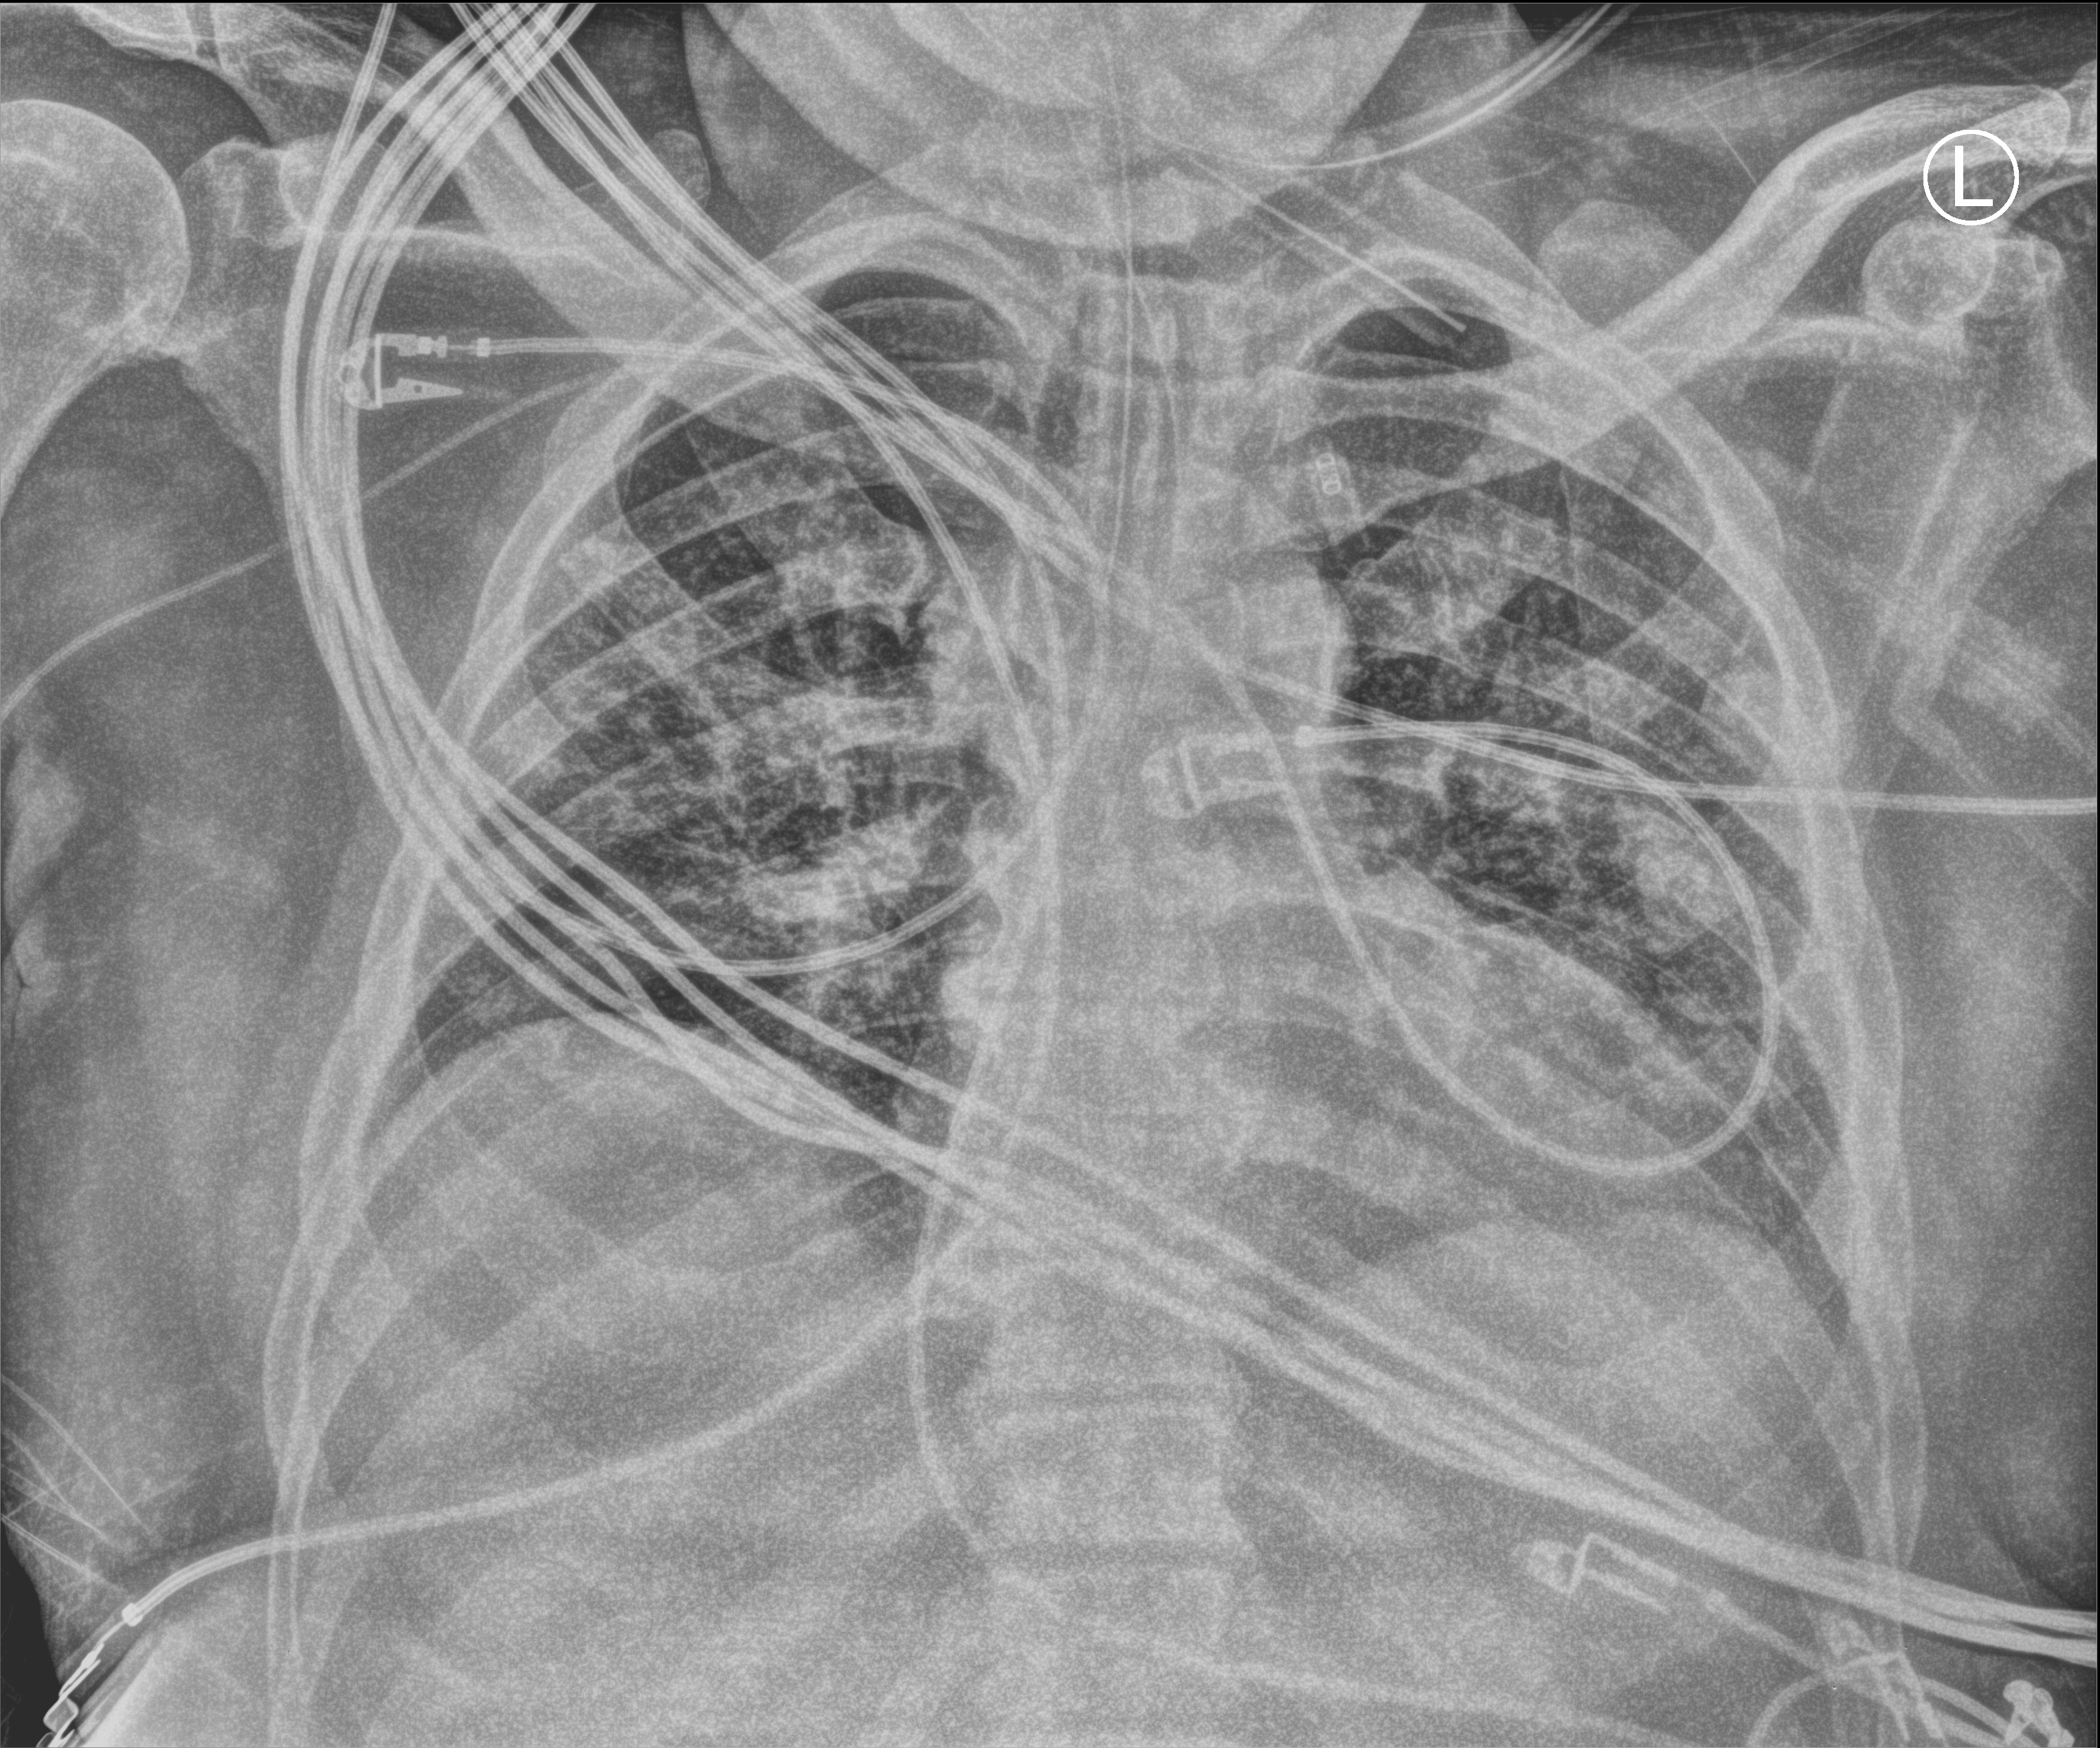
Bedside chest radiograph (computed radiography), anteroposterior (AP) projection. Patient hospitalised with COVID-19; male, aged 18–59 years.
Admission-level facts for this patient (not findings on this image; timing relative to this image not recorded): admitted to intensive care during this hospital stay: yes; mechanically ventilated during this hospital stay: yes; smoking status (admission record): never.